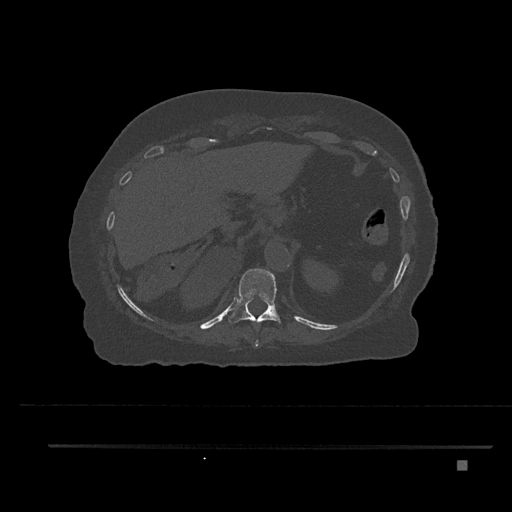
CT including the spine, one axial slice. Slice 314 of 797 in the series (ordered by position). Reconstruction kernel Br40s/3. 120 kVp. Bone window (W 1800 / L 400 HU). 0.5 mm slice thickness. 512 × 512 image matrix, field of view 437 × 437 mm. Patient: female, 76 years. Case-level facts recorded for this patient, not image findings: primary cancer: lung.
Outlined on this slice (semi-automatic segmentation, software-assisted and operator-edited):
- T10 vertebra: box from (x=254, y=339) to (x=259, y=347) px
- T11 vertebra: (x=228, y=269)–(x=282, y=325)